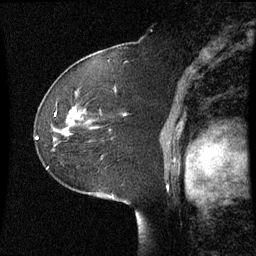
Breast MRI (dynamic contrast-enhanced), one sagittal slice. Slice 43 of 60 in the series (ordered by position). Dynamic contrast-enhanced series, image 2 of 3 at this slice position (ordered by acquisition). 1.5 T. TE 4.2 ms, TR 8.9 ms. 2.2 mm slice thickness. 256 × 256 image matrix. Patient: female, 51 years. From the clinical record (not read from this slice): setting: breast cancer imaged before/during neoadjuvant chemotherapy; receptor status: HR-positive, HER2-negative.
Outlined on this slice (semi-automatically segmented with operator editing):
- analysis volume of interest (the breast-tissue region the enhancement analysis was run in; not a lesion): bounding box [x1, y1, x2, y2] px = [54, 108, 97, 151]
- tumour enhancement mask (voxels above the 70 % enhancement threshold inside the analysis volume of interest): [68, 114, 81, 123]